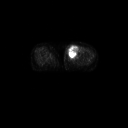
FDG PET of an extremity soft-tissue mass (from a PET/CT study), one axial slice; slice 41 of 91 in the series (ordered by position); 3.27 mm slice thickness; 128 × 128 image matrix, field of view 700 × 700 mm. Female patient, age 74 years. From the clinical record (not read from this slice): histological type: pleomorphic leiomyosarcoma; grade: high; site of the primary tumour: left thigh.
Annotated regions visible in this slice (expert contour drawn on MRI and transferred to this co-registered scan by the dataset authors):
- gross tumour volume including surrounding oedema: box from (x=65, y=44) to (x=80, y=61) px
- gross tumour volume (mass): (x=67, y=44)–(x=79, y=59)